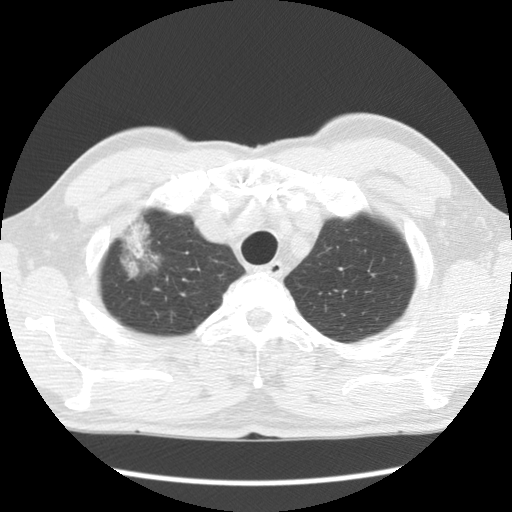
Chest CT (low-dose screening protocol), one axial image; baseline screening round; lung window (W 1500 / L -600 HU); standard (soft-tissue) reconstruction kernel (STANDARD); slice 16 of 132 in the series; 512 × 512 image matrix. Male participant, aged 64 years at enrolment.
- Lesion marked by an expert reader, bounding box (x1, y1, x2, y2) in pixels: (105, 213, 172, 281).
- The screening reader recorded 2 non-calcified nodules or masses ≥4 mm on this exam (right upper lobe, left upper lobe); which of them this box marks is not recorded.
- Official screen result: positive, change unspecified: nodule(s) >= 4 mm or enlarging nodule(s), mass(es), or other non-specific abnormalities suspicious for lung cancer.
- Lung cancer was diagnosed 750 days after this screen (after the third annual screen): adenocarcinoma, NOS, right upper lobe, well differentiated (G1), stage IB (AJCC 6th edition), 45 mm at pathology.